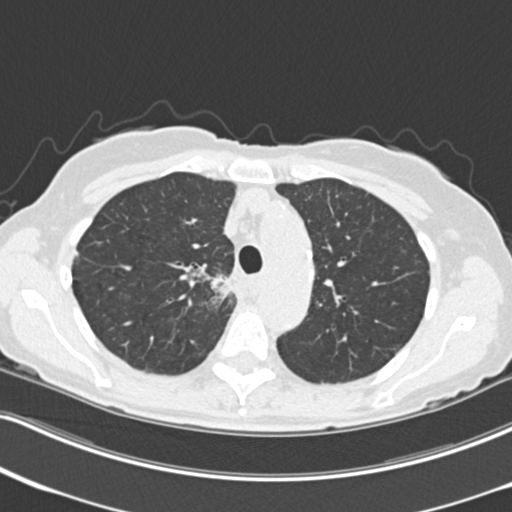
Axial slice from a low-dose chest CT screening exam; third screening round (two years after baseline); lung window (W 1500 / L -600 HU); standard (soft-tissue) reconstruction kernel (B30f); slice 61 of 226 in the series; 512 × 512 image matrix. Female participant, aged 68 years at enrolment. Current smoker at enrolment.
- Lesion marked by an expert reader, bounding box (x1, y1, x2, y2) in pixels: (195, 268, 248, 324).
- Screening reader's record for this exam (one nodule recorded; not confirmed to be the boxed lesion): non-calcified nodule or mass ≥4 mm, right upper lobe, 31 × 29 mm, poorly defined margins, soft tissue attenuation, pre-existing on the prior screen: no.
- Official screen result: positive, other.
- Participant outcome: lung cancer diagnosed 79 days after this screen — squamous cell carcinoma, NOS, right upper lobe, mediastinum, poorly differentiated (G3), stage IIIB (AJCC 6th edition), 43 mm at pathology.